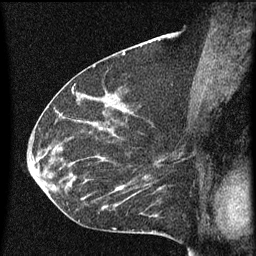
Breast MRI (dynamic contrast-enhanced), one sagittal slice; slice 33 of 60 in the series (ordered by position); dynamic contrast-enhanced series, image 2 of 3 at this slice position (ordered by acquisition); 1.5 T; TE 4.2 ms, TR 8 ms; 256 × 256 image matrix, field of view 180 × 180 mm. Female patient, age 55 years.
Structures marked on this image (semi-automatic segmentation, software-assisted and operator-edited):
- analysis volume of interest (the breast-tissue region the enhancement analysis was run in; not a lesion): bounding box (x1, y1, x2, y2) in pixels: (51, 156, 145, 217)
- tumour enhancement mask (voxels above the 70 % enhancement threshold inside the analysis volume of interest): (53, 160, 145, 215)